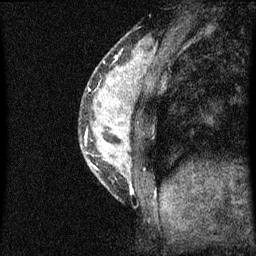
Breast MRI (dynamic contrast-enhanced), one sagittal slice; position 20 of 60 along the scan axis; dynamic contrast-enhanced series, image 2 of 3 at this slice position (ordered by acquisition); 1.5 T; TE 4.2 ms, TR 8 ms; 2 mm slice thickness; 256 × 256 image matrix, field of view 180 × 180 mm. Patient: female, 33 years.
Annotated regions visible in this slice (semi-automatically segmented with operator editing):
- analysis volume of interest (the breast-tissue region the enhancement analysis was run in; not a lesion): box from (x=80, y=56) to (x=151, y=195) px
- tumour enhancement mask (voxels above the 70 % enhancement threshold inside the analysis volume of interest): (x=85, y=68)–(x=134, y=195)